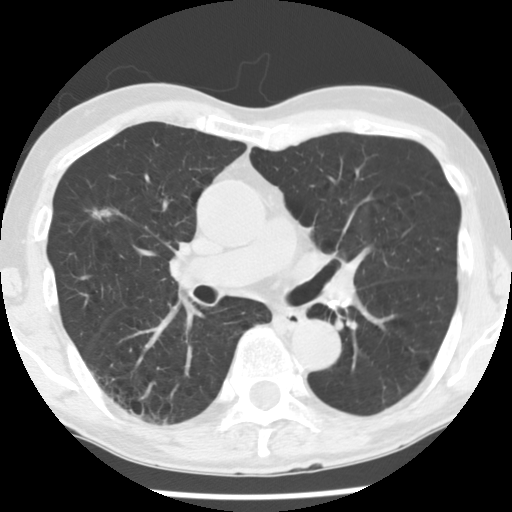
Low-dose screening chest CT, one axial slice; slice 98 of 176 in the series (ordered by position); reconstruction kernel STANDARD; lung window (W 1500 / L -600 HU); 2.5 mm slice thickness; 512 × 512 image matrix, field of view 309 × 309 mm.
Structures marked on this image (manually delineated by an expert):
- lesion 1 (tumor, upper lobe of right lung): box from (x=92, y=209) to (x=112, y=220) px